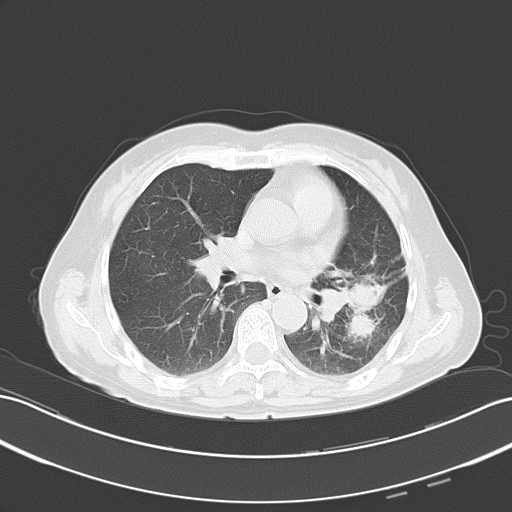
Chest CT, one axial slice; position 27 of 51 along the scan axis; reconstruction kernel B70f; 120 kVp; lung window (W 1500 / L -600 HU); 512 × 512 image matrix. Female patient, age 54 years. Case-level facts recorded for this patient, not image findings: clinical TNM (as recorded): T3 N1 M0.
Outlined on this slice (rectangle marked by the reading radiologist):
- lung tumour (recorded histology: adenocarcinoma): box from (x=345, y=276) to (x=389, y=344) px